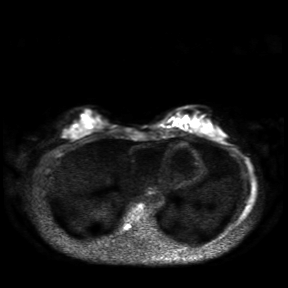
Breast MRI, one axial slice. Position 8 of 30 along the scan axis. Diffusion-weighted series; image 2 of 4 stored at this slice position (different b-values; order by instance number). 3 T. 4 mm slice thickness. 288 × 288 image matrix, field of view 360 × 360 mm. Female patient.
Annotated regions visible in this slice (outlined manually by an expert reader):
- tumour on diffusion-weighted imaging: bounding box [x1, y1, x2, y2] px = [174, 115, 183, 121]